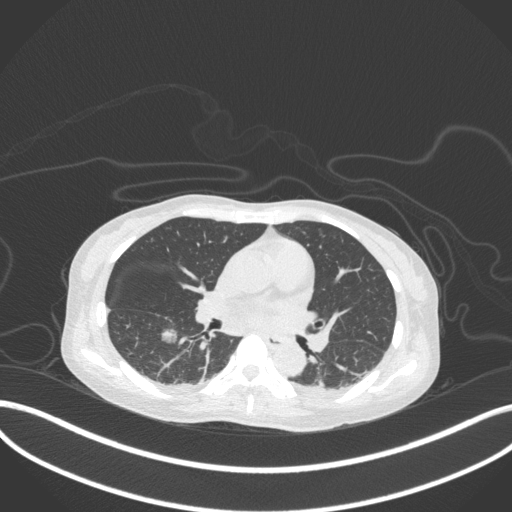
Chest CT, one axial slice; slice 162 of 260 in the series (ordered by position); reconstruction kernel B31f; 120 kVp; lung window (W 1500 / L -600 HU); 1 mm slice thickness; 512 × 512 image matrix, field of view 400 × 400 mm. Female patient, age 44 years. From the clinical record (not read from this slice): clinical TNM (as recorded): T1c N0 M0.
Structures marked on this image (bounding box drawn by a radiologist):
- lung tumour (recorded histology: adenocarcinoma): bounding box (x1, y1, x2, y2) in pixels: (158, 323, 180, 348)